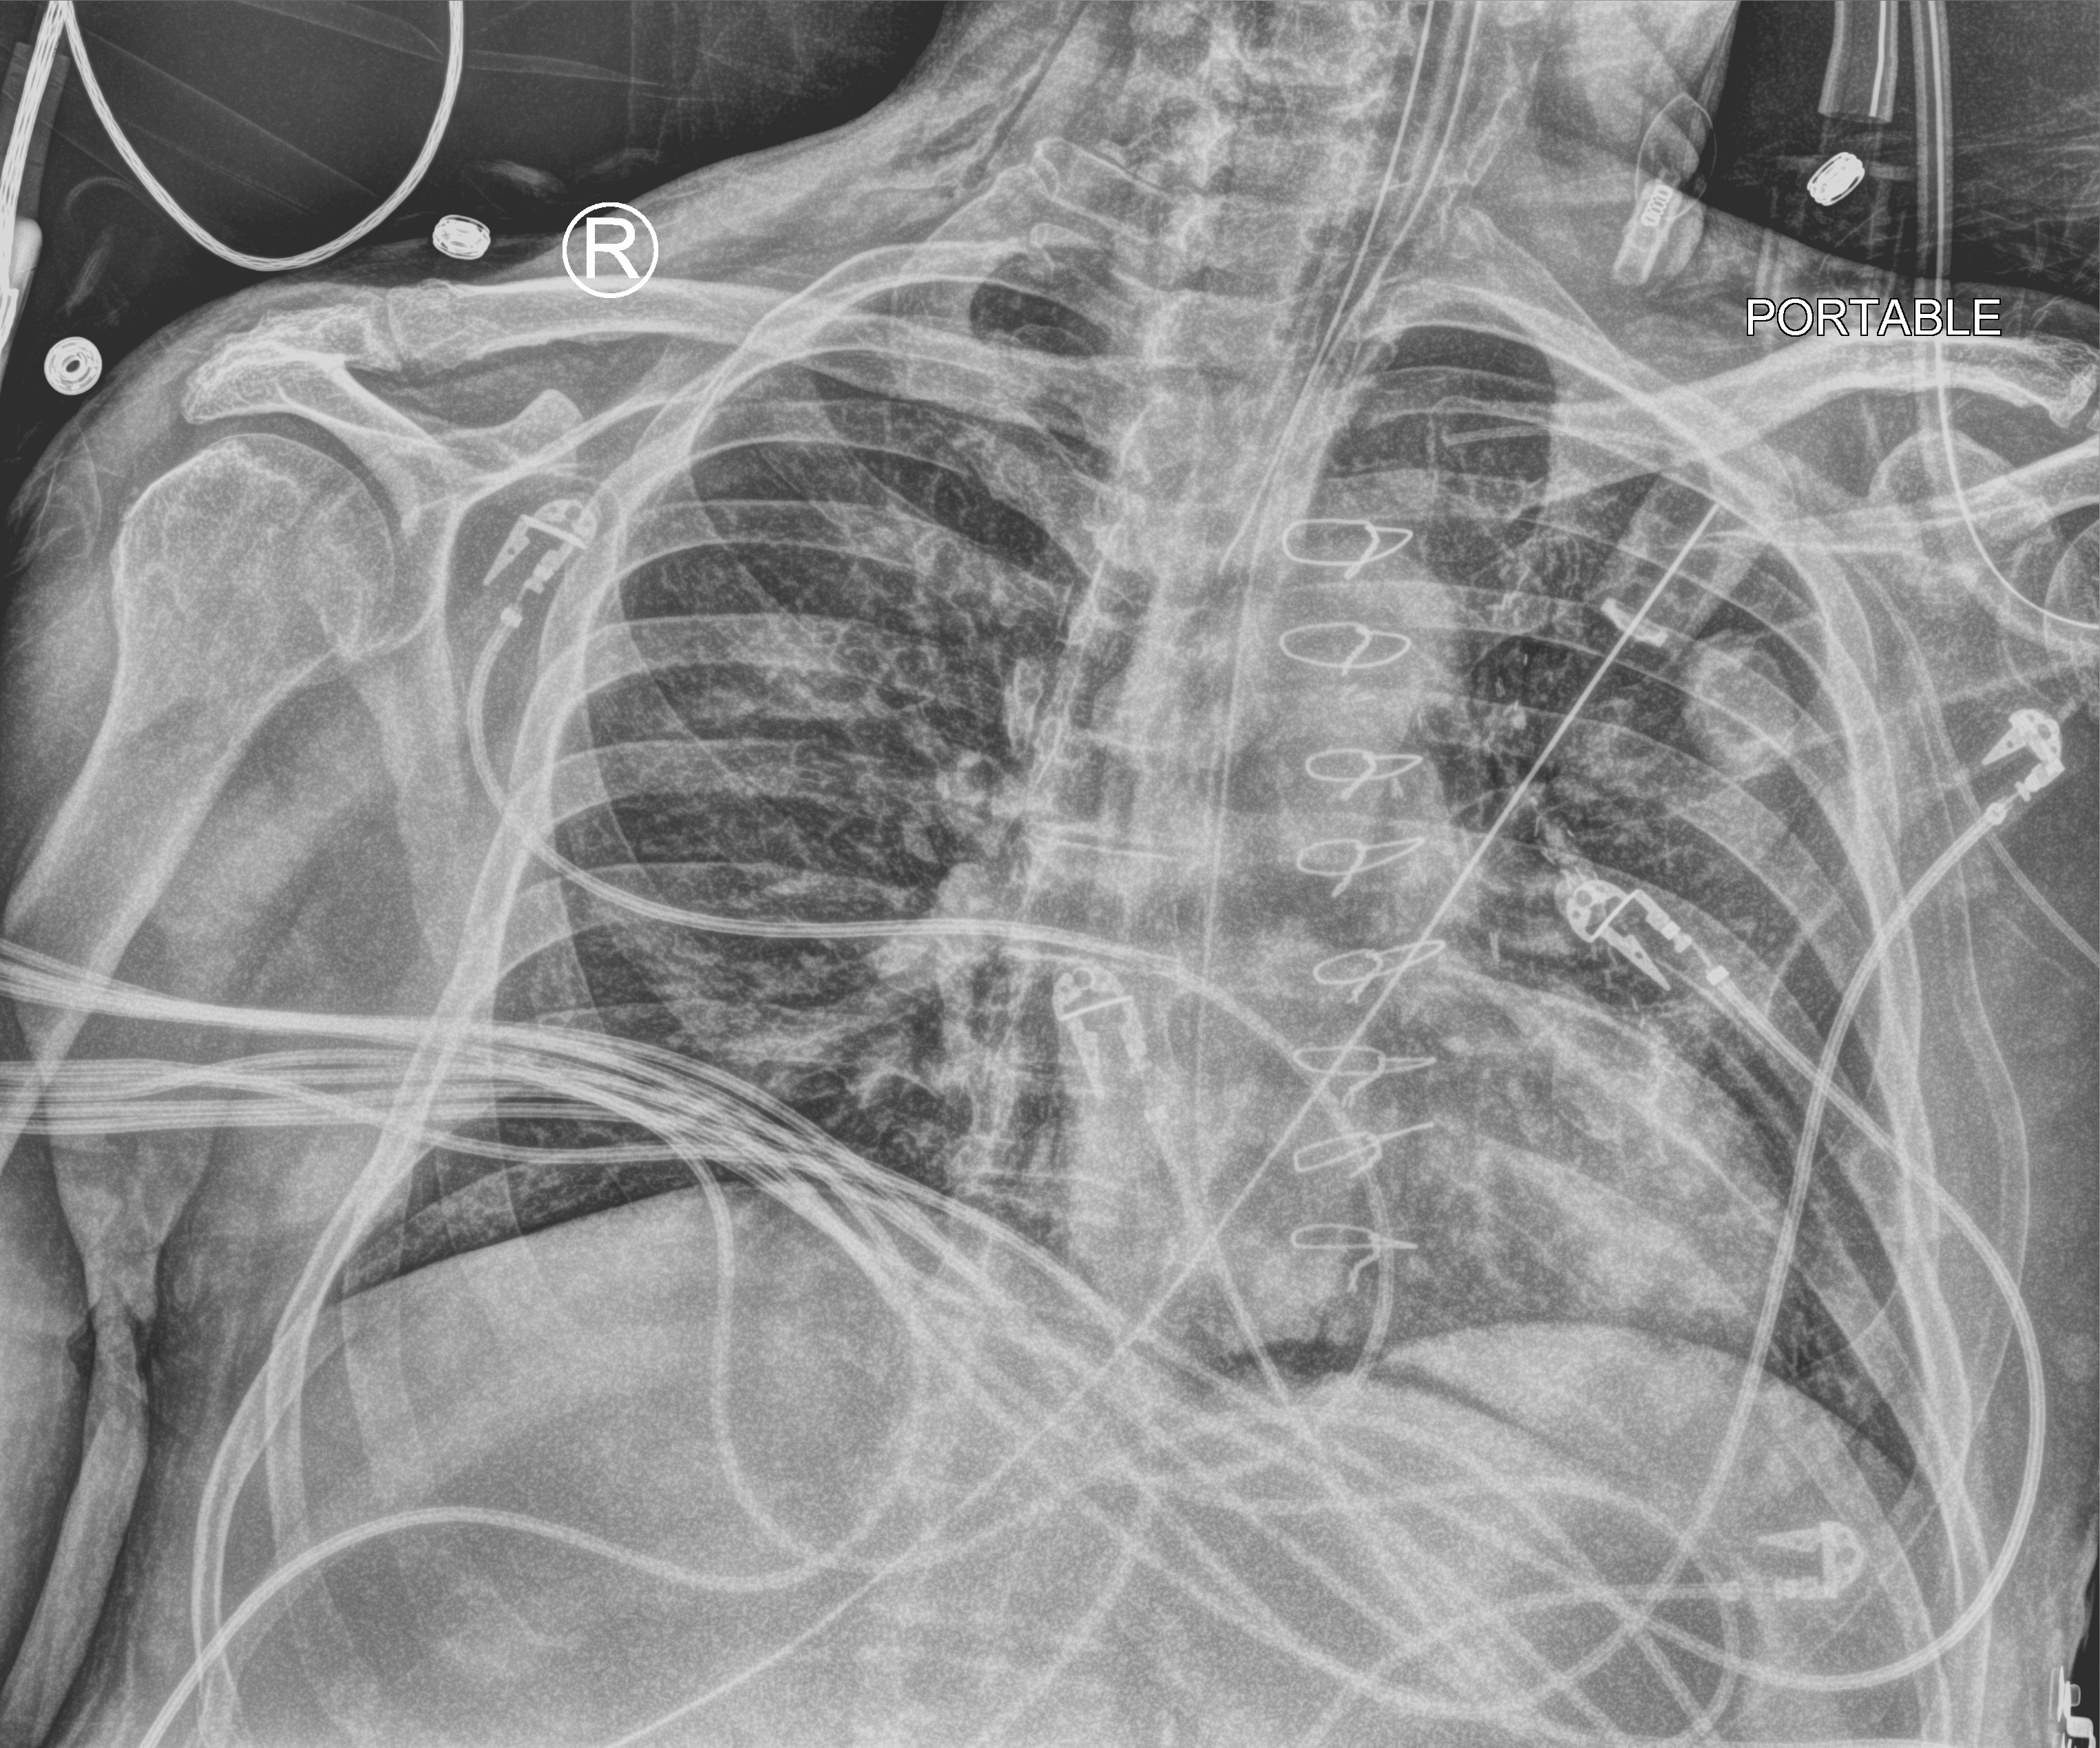
Bedside chest radiograph (computed radiography). Male patient hospitalised with COVID-19, age 60–74 years.
From the hospital-stay record, not from the radiograph (when in the stay this image was taken is not recorded): admitted to intensive care during this hospital stay: yes; mechanically ventilated during this hospital stay: yes; hypertension (admission record): yes.